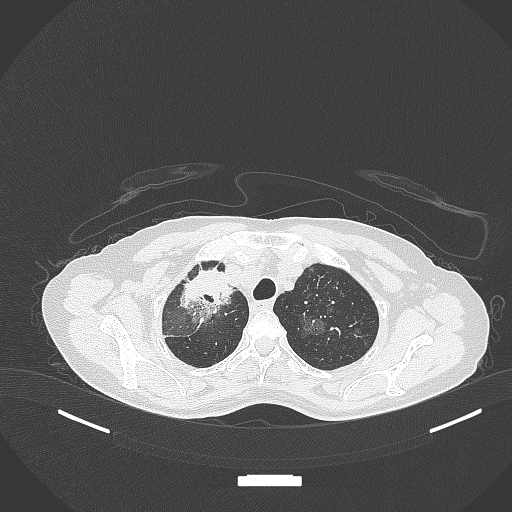
Chest CT, one axial slice. Position 272 of 284 along the scan axis. 120 kVp. Lung window (W 1500 / L -600 HU). 1 mm slice thickness. 512 × 512 image matrix, field of view 400 × 400 mm. Female patient, age 59 years. From the clinical record (not read from this slice): clinical TNM (as recorded): T3 N0 M0; histopathological grade: G1.
Structures marked on this image (rectangle marked by the reading radiologist):
- lung tumour (recorded histology: adenocarcinoma): bounding box [x1, y1, x2, y2] px = [180, 265, 238, 325]